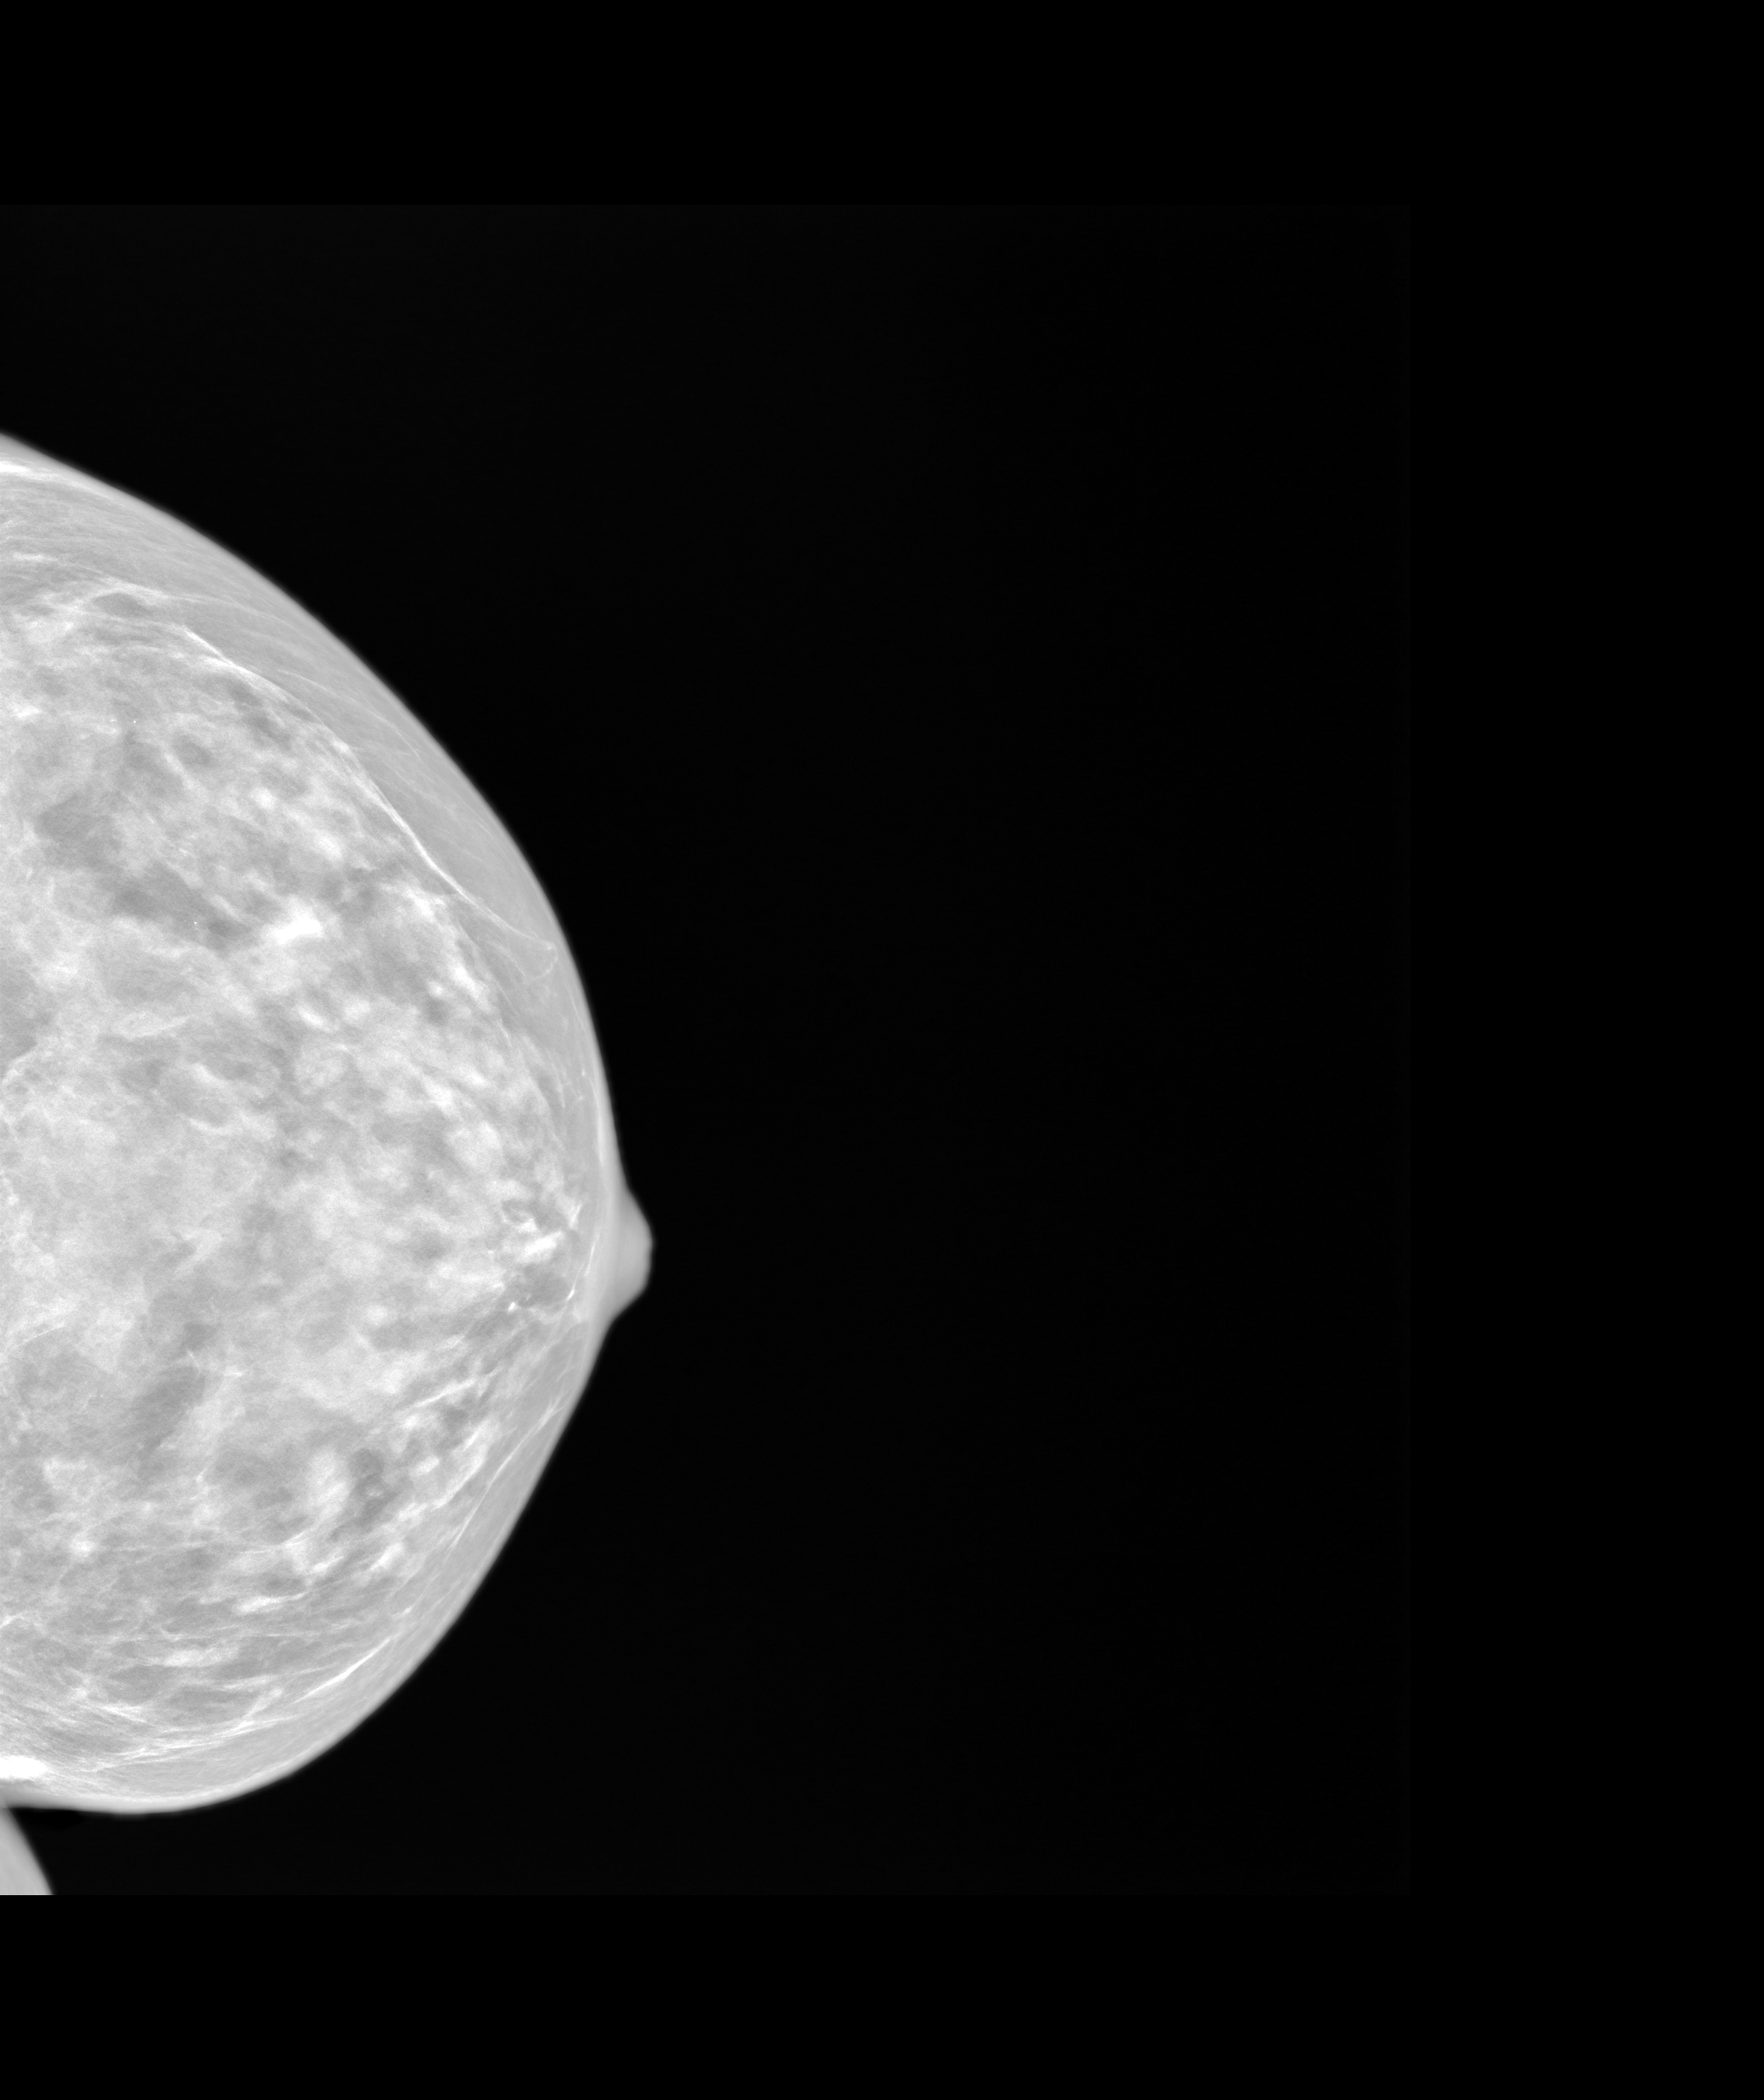
Synthetic 2-D view generated from a tomosynthesis acquisition (not an FFDM exposure), left breast, CC view, screening examination, system: SenoIris_1SP1.2(425). Patient: female, 73 years.
BI-RADS breast density category at the screening exam (both breasts, scale 1–4): 4. Final BI-RADS assessment for this screening round (tomosynthesis exam, both breasts): category 1. Recall: no recall after this screen.